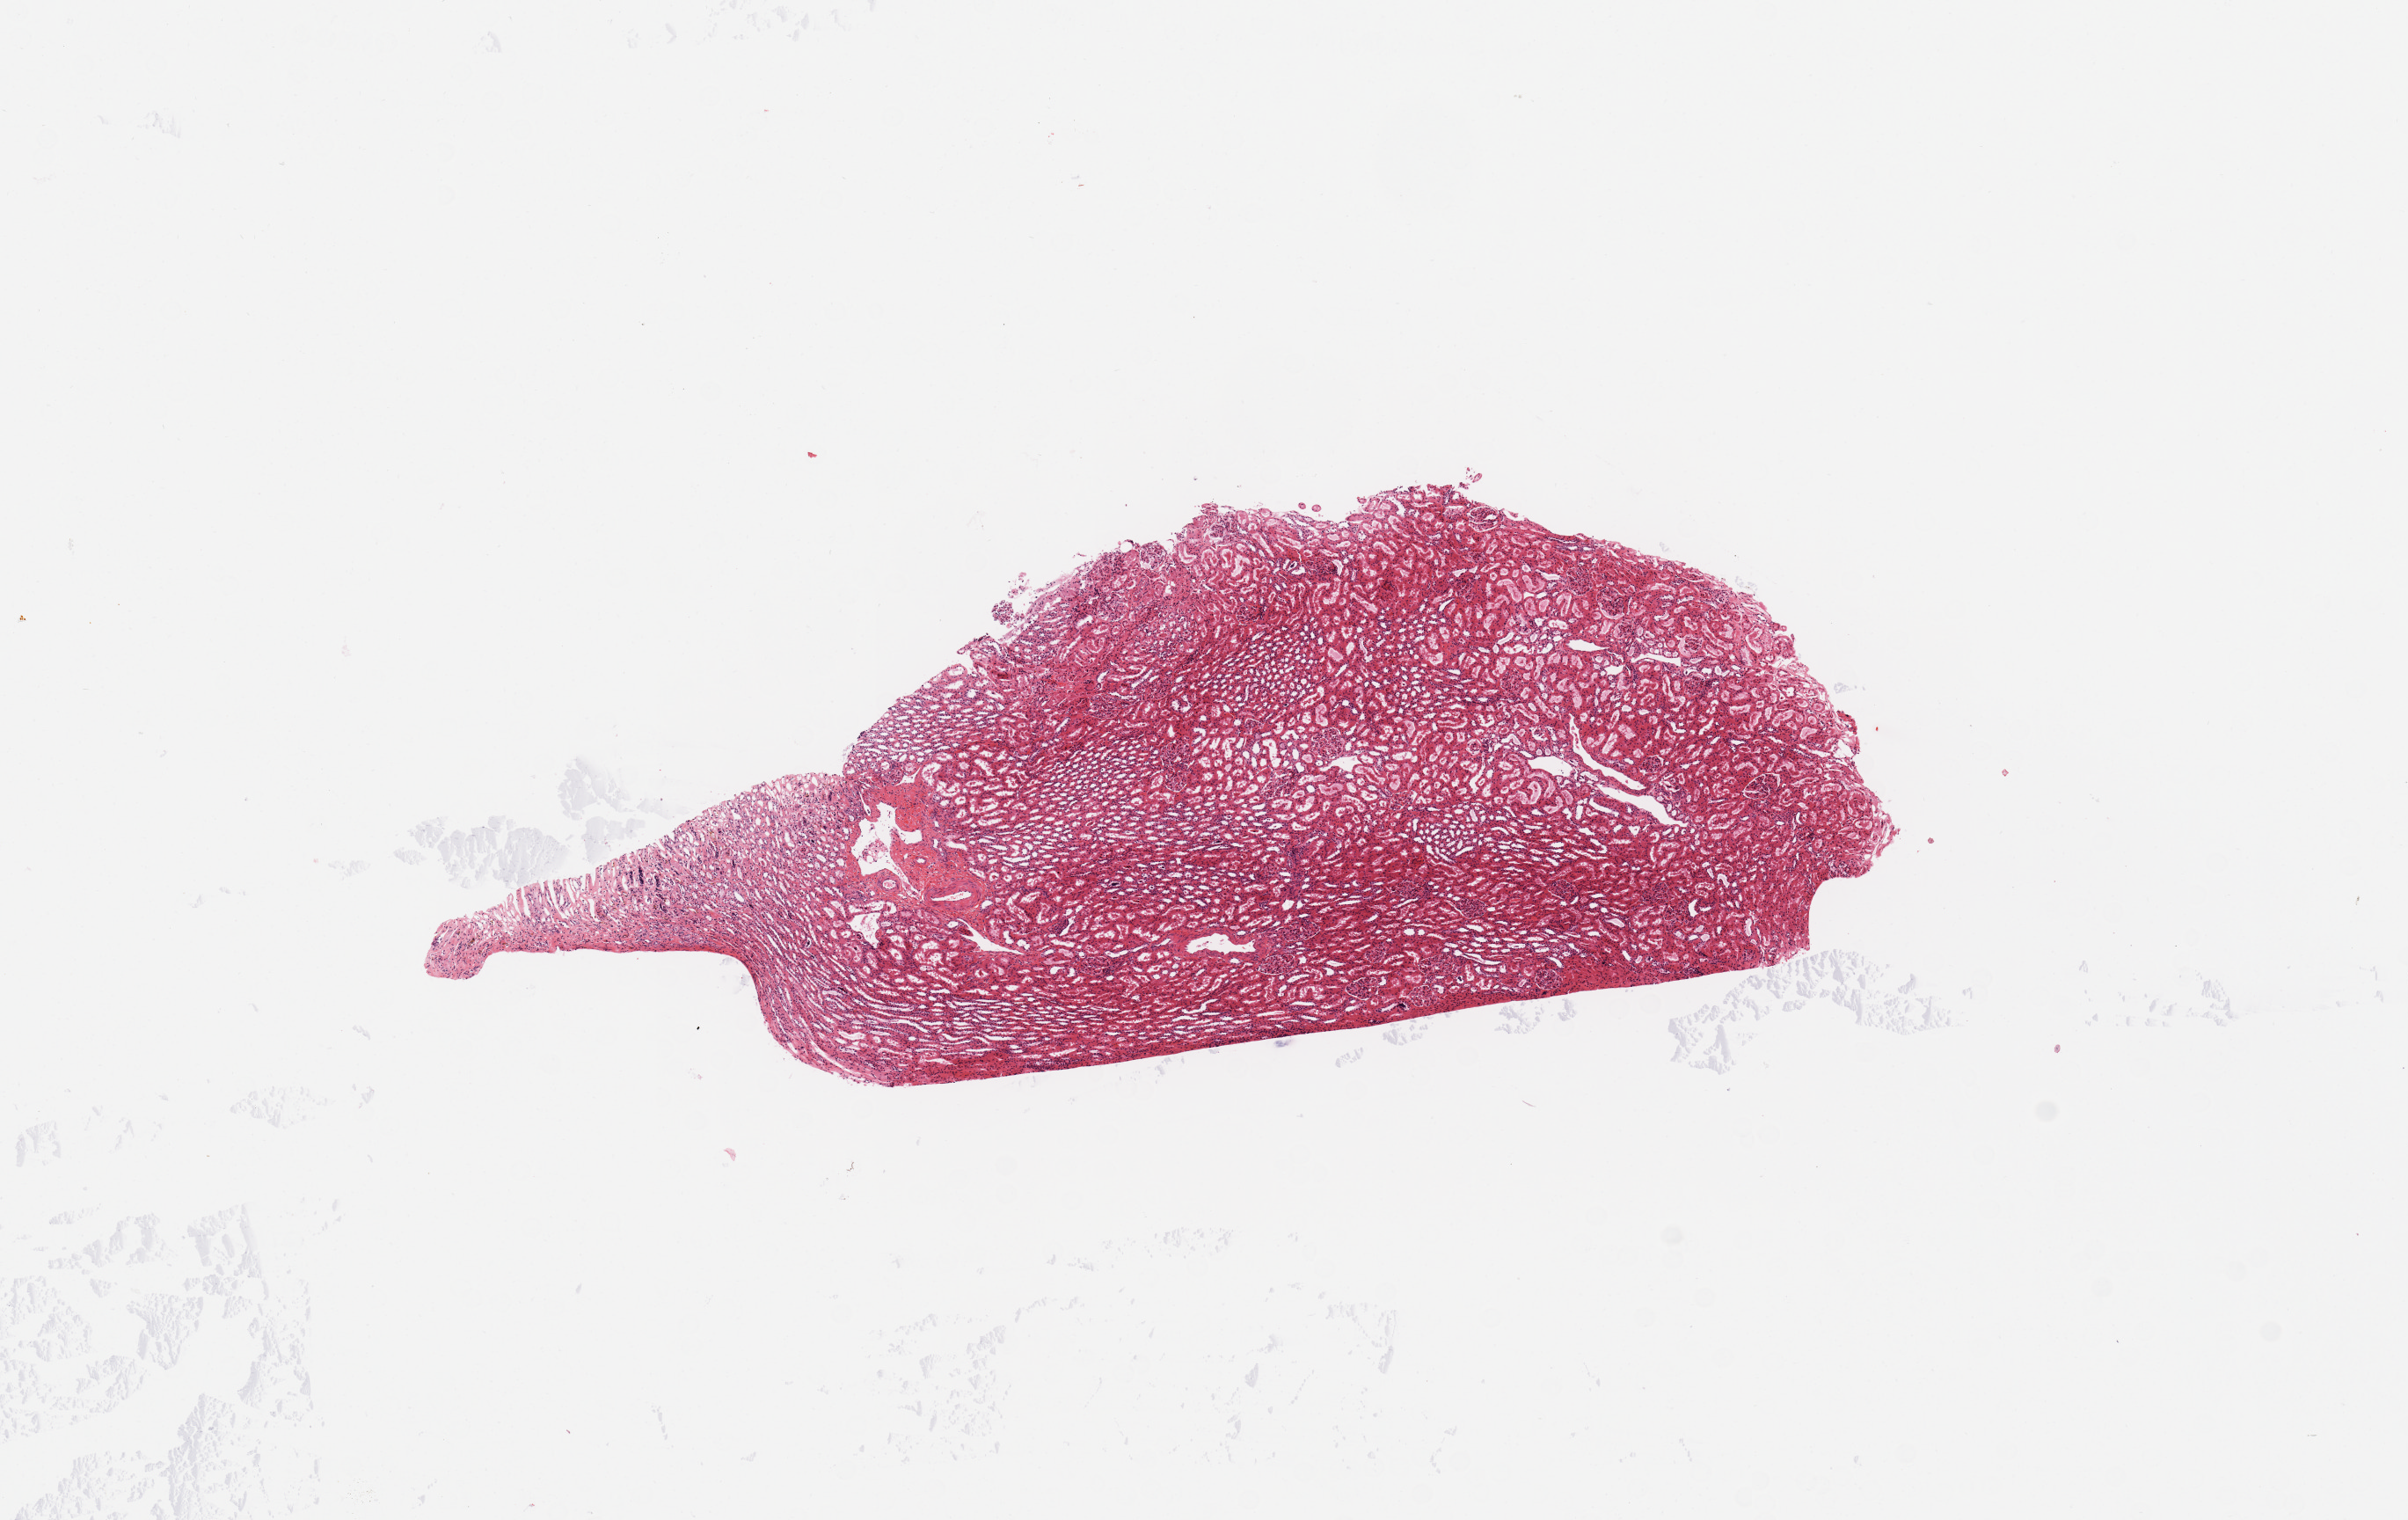
H&E whole-slide image — whole scanned area (about 10.8 x 6.8 mm, acquisition: 20x scan) shown as a low-resolution overview. Normal (non-tumour) tissue sample, kidney. Female, 47 y/o.
This section: normal (non-tumour) tissue from the same patient. Patient diagnosis: Renal cell carcinoma, NOS.